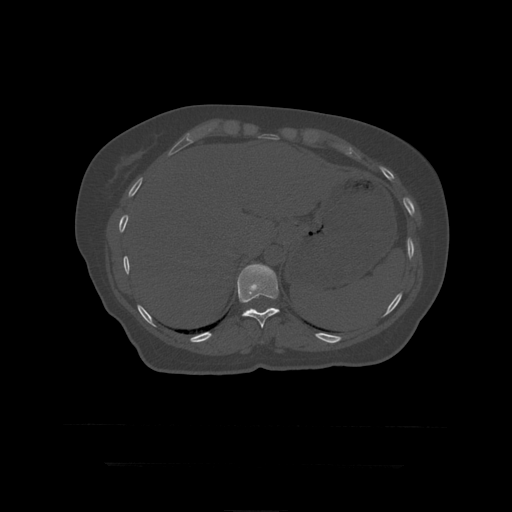
CT including the spine, one axial slice. Position 217 of 399 along the scan axis. 120 kVp. Bone window (W 1800 / L 400 HU). 512 × 512 image matrix, field of view 450 × 450 mm. Patient age 41 years. Case-level facts recorded for this patient, not image findings: primary cancer: breast.
Structures marked on this image (semi-automatically segmented with operator editing):
- T11 vertebra: bounding box <237,264,280,329> (left, top, right, bottom; pixels)
- T12 vertebra: <247,309,279,311>